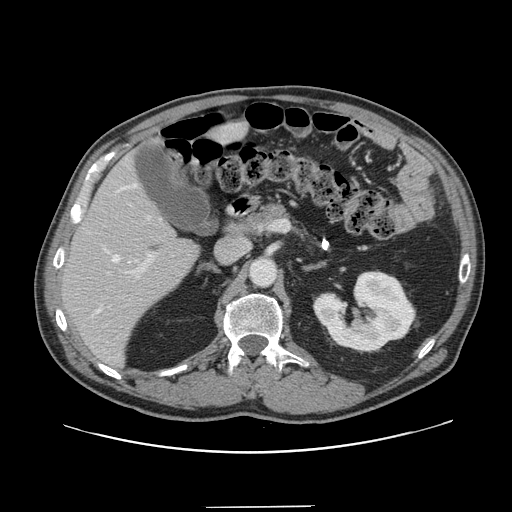
Contrast-enhanced abdominal CT, one axial slice. Position 80 of 139 along the scan axis. Intravenous contrast given. Soft-tissue window (W 400 / L 40 HU). 2.5 mm slice thickness. 512 × 512 image matrix, field of view 397 × 397 mm. Male patient, age 64 years. Case-level facts recorded for this patient, not image findings: diagnosis: colorectal cancer liver metastases, imaged before liver resection; multiple liver metastases: yes; largest metastasis: 3.5 cm; chemotherapy before resection: yes.
Outlined on this slice (outlined manually by an expert reader):
- hepatic veins: box from (x=96, y=184) to (x=161, y=313) px
- liver: (x=63, y=124)–(x=243, y=366)
- planned liver remnant (the part of the liver to remain after resection): (x=62, y=124)–(x=243, y=365)
- portal vein (with intrahepatic branches): (x=127, y=254)–(x=153, y=278)